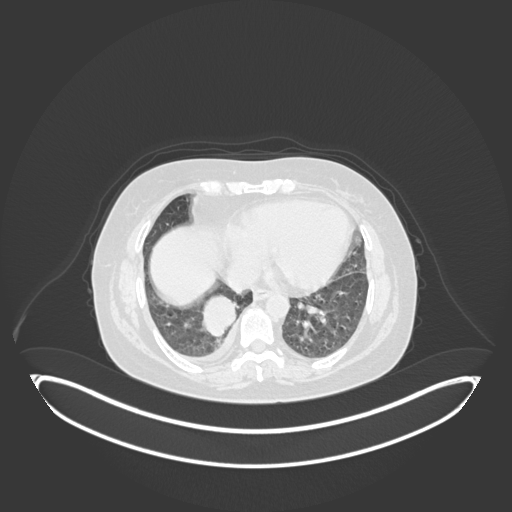
Chest CT, one axial slice. Slice 46 of 231 in the series (ordered by position). Reconstruction kernel B30f. 120 kVp. Lung window (W 1500 / L -600 HU). 1 mm slice thickness. 512 × 512 image matrix, field of view 500 × 500 mm. Female patient, age 56 years. From the clinical record (not read from this slice): clinical TNM (as recorded): T2b N1 M0; histopathological grade: G3.
Structures marked on this image (bounding box drawn by a radiologist):
- lung tumour (recorded histology: small cell carcinoma): bounding box (x1, y1, x2, y2) in pixels: (198, 290, 244, 348)